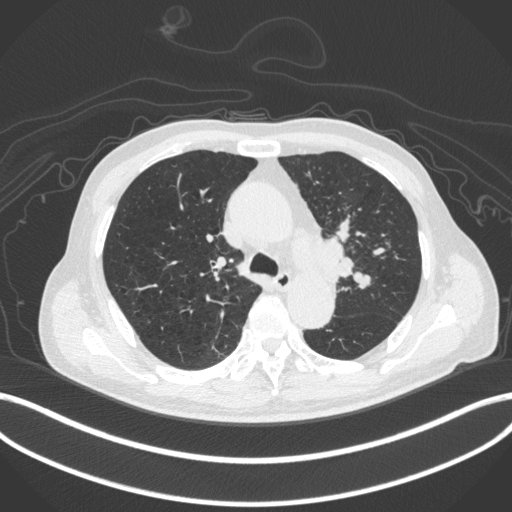
Chest CT, one axial slice. Position 298 of 420 along the scan axis. Reconstruction kernel B31f. Lung window (W 1500 / L -600 HU). 1 mm slice thickness. 512 × 512 image matrix, field of view 400 × 400 mm. Patient: male, 77 years. From the clinical record (not read from this slice): clinical TNM (as recorded): T3 N1 M0.
Outlined on this slice (bounding box drawn by a radiologist):
- lung tumour (recorded histology: adenocarcinoma): box from (x=304, y=223) to (x=359, y=282) px